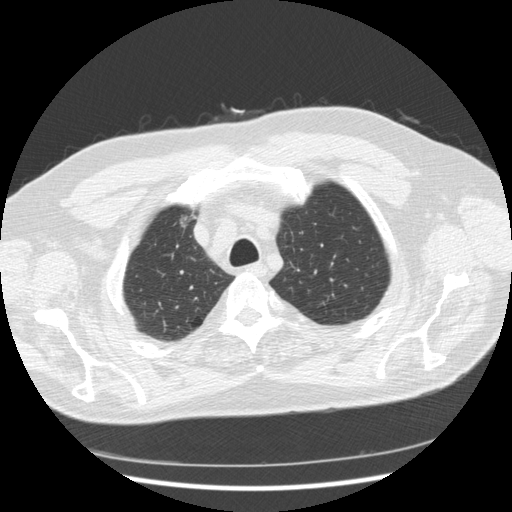
Axial slice from a low-dose chest CT screening exam; second annual screen; lung window (W 1500 / L -600 HU); standard (soft-tissue) reconstruction kernel (STANDARD); 512 × 512 image matrix. Male participant, aged 66 years at enrolment. Former smoker at enrolment.
Expert-annotated lung lesion, bounding box <156,204,205,242> (left, top, right, bottom; pixels). Screening reader's record for this exam: no non-calcified nodule ≥4 mm recorded. Official screen result: positive, other. Lung cancer was diagnosed 603 days after this screen: bronchiolo-alveolar adenocarcinoma, NOS, right upper lobe, moderately differentiated (G2), stage IA (AJCC 6th edition), 12 mm at pathology.